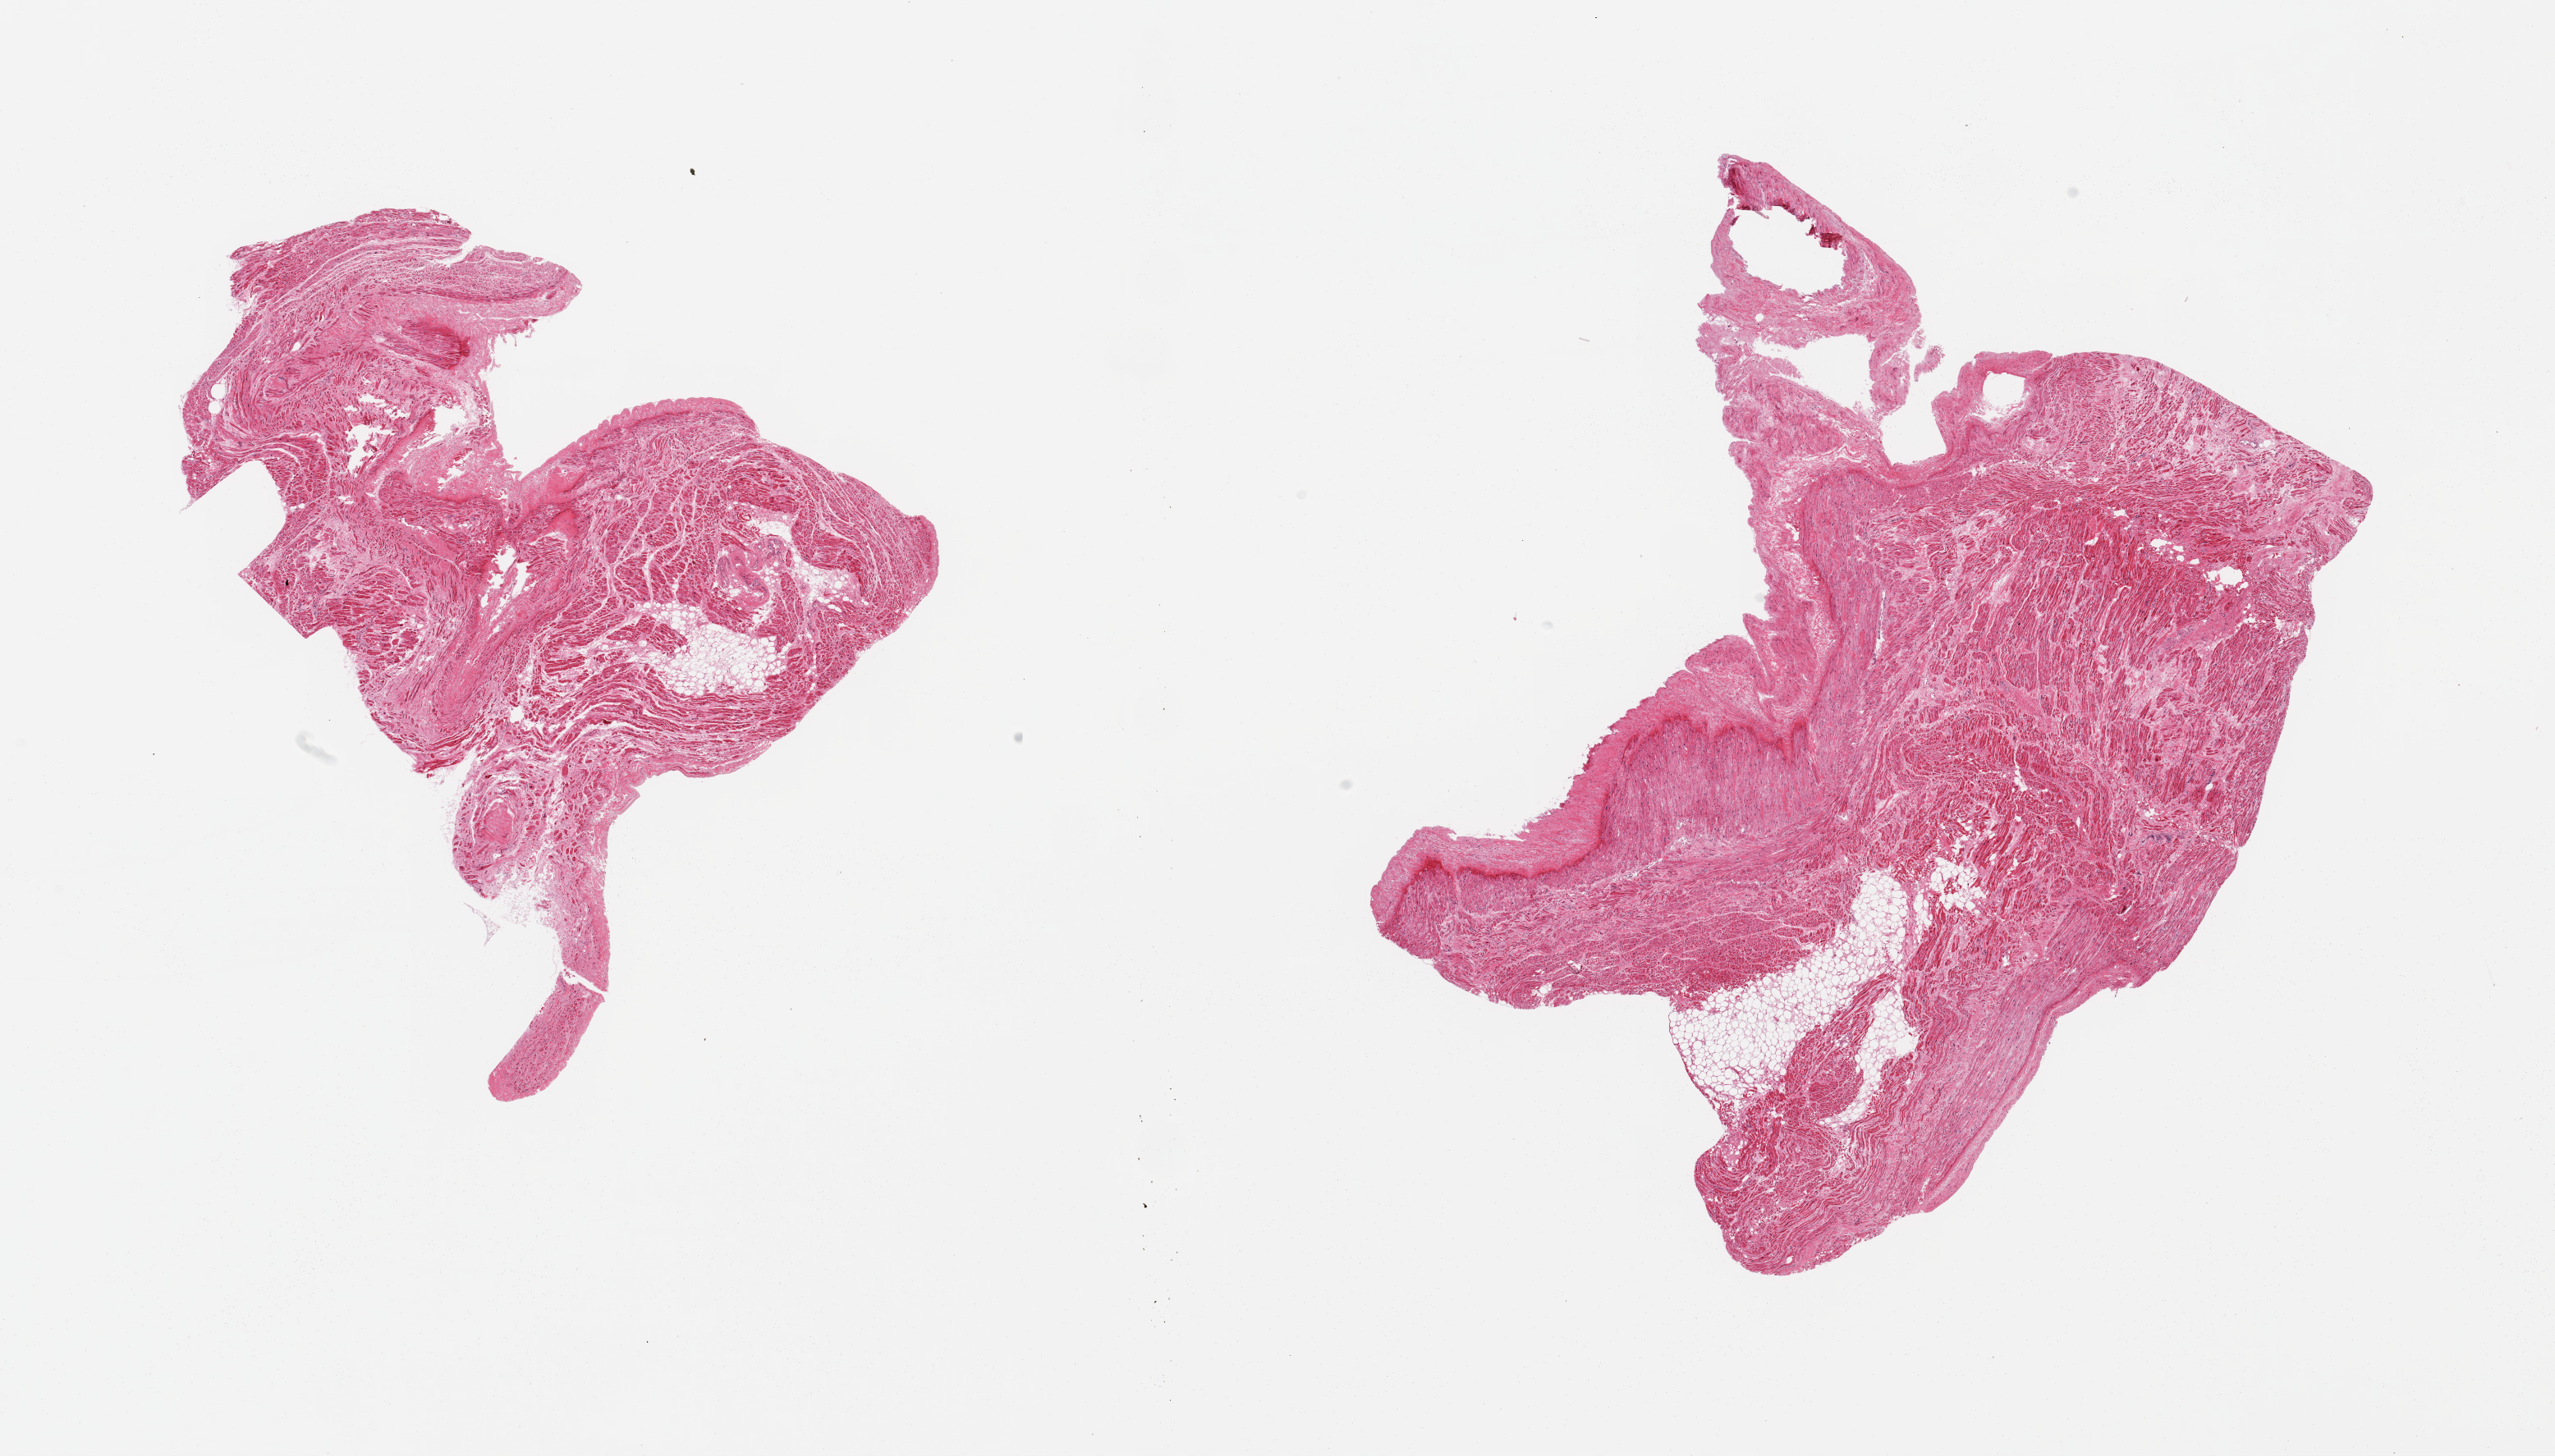
Haematoxylin and eosin whole-slide image — shown as a low-resolution overview of the whole scanned area (about 24.6 x 14.0 mm, slide scanned at 20x), PAXgene-fixed paraffin-embedded (PFPE) section, section of auricular appendage (target tissue), tissue donor sample. Donor: male.
Reviewer comment on this tissue sample: 2 pieces, no abnormalities.